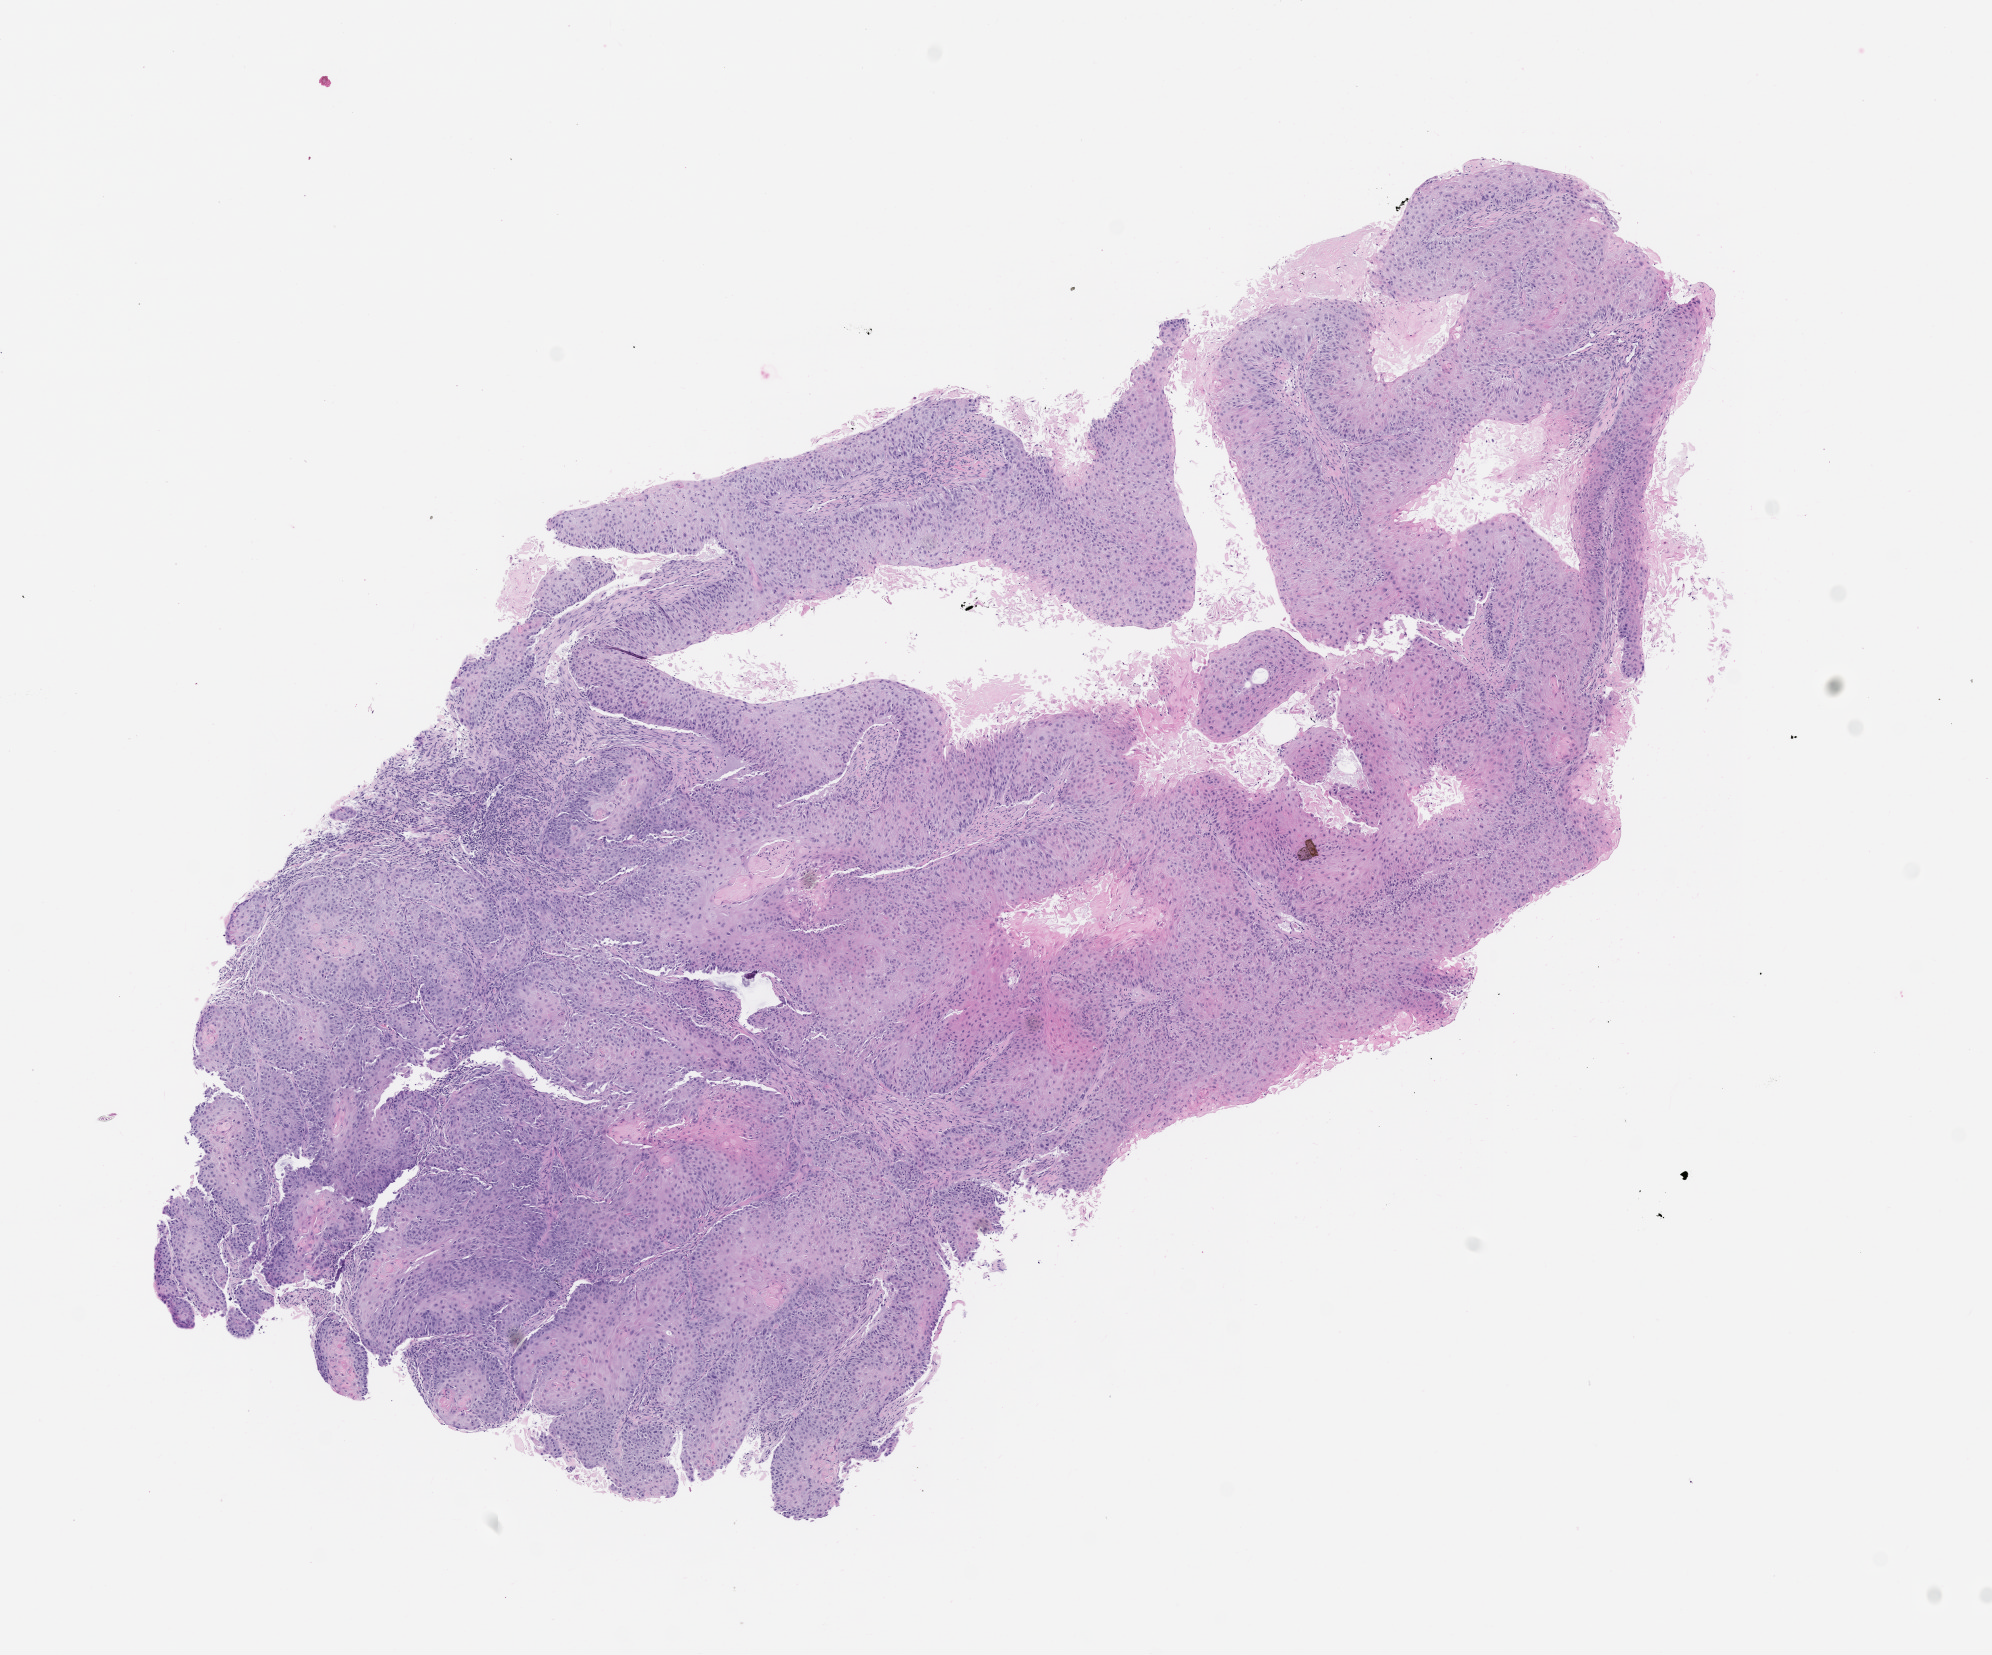
H&E whole-slide image of a patient-derived xenograft (PDX) tumor grown in a mouse, passage 3, shown as a low-resolution overview of the whole scanned area (about 8.0 x 6.7 mm). Formalin-fixed, paraffin-embedded (FFPE) tissue. Tumor site category: lung.
Originating patient diagnosis: Lung Squamous Cell Carcinoma.